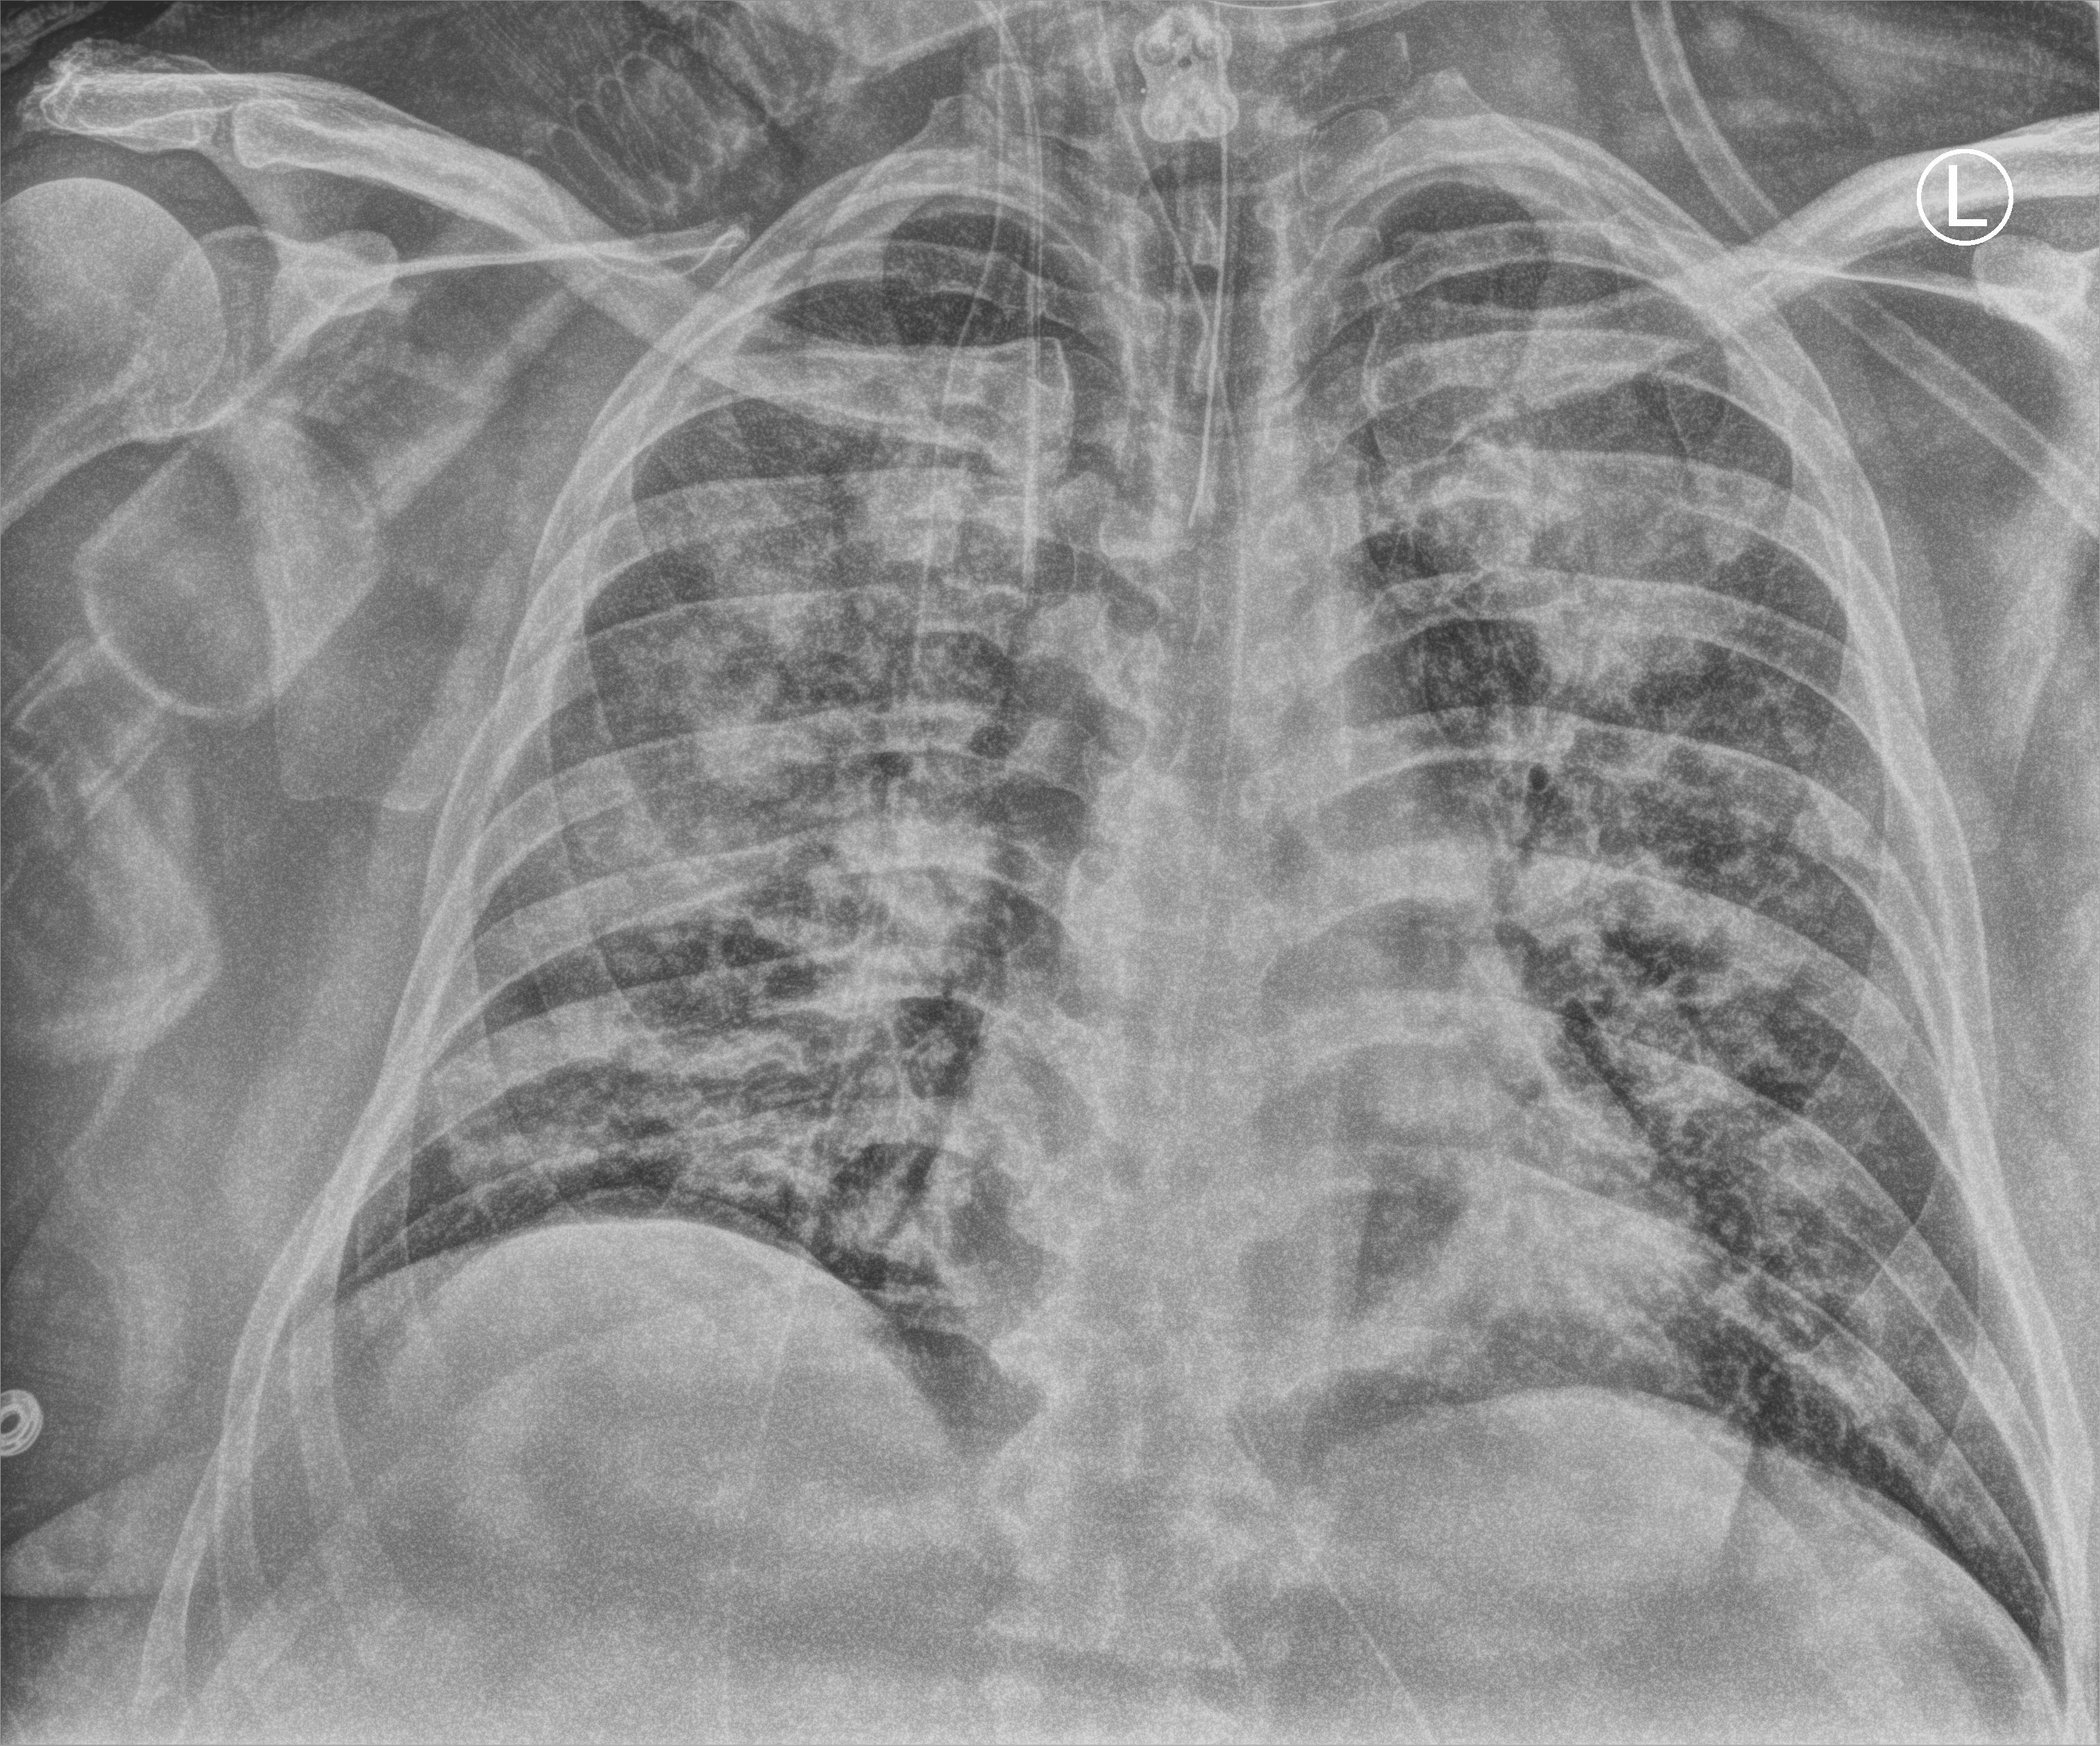
Chest X-ray (portable). Male patient hospitalised with COVID-19, age 18–59 years.
From the hospital-stay record, not from the radiograph (when in the stay this image was taken is not recorded): chronic kidney disease (admission record): no; admitted to intensive care during this hospital stay: yes; length of hospital stay: 47 days.